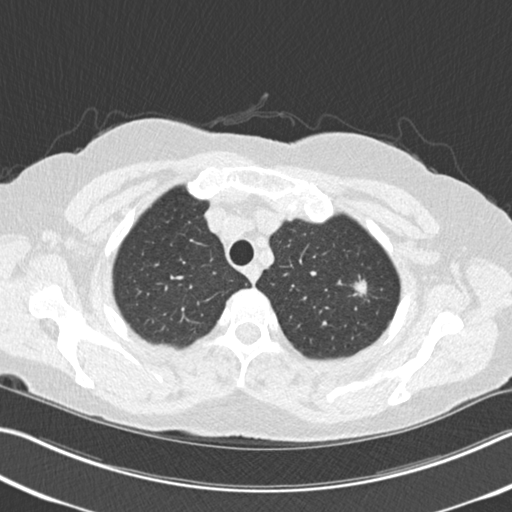
Axial slice from a low-dose chest CT screening exam, second annual screen, lung window (W 1500 / L -600 HU). Female participant, aged 64 years at enrolment. Former smoker at enrolment.
Expert reader's lesion annotation, bounding box <345,270,379,303> (left, top, right, bottom; pixels). The exam's reader record, not a measurement of the box and not confirmed to be the same lesion: non-calcified nodule or mass ≥4 mm, left upper lobe, 13 × 10 mm, spiculated (stellate) margins, soft tissue attenuation, pre-existing on the prior screen: yes; interval growth: yes.